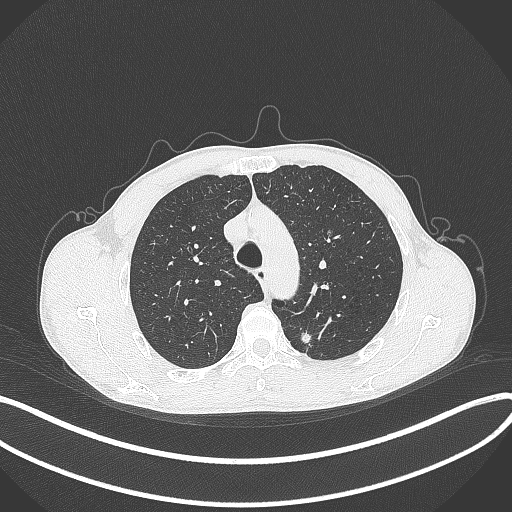
Chest CT, one axial slice. Slice 303 of 429 in the series (ordered by position). Lung window (W 1500 / L -600 HU). 512 × 512 image matrix, field of view 400 × 400 mm. Male patient, age 51 years. From the clinical record (not read from this slice): clinical TNM (as recorded): T2a N1 M1.
Outlined on this slice (bounding box drawn by a radiologist):
- lung tumour (recorded histology: adenocarcinoma): bounding box (x1, y1, x2, y2) in pixels: (297, 325, 315, 352)